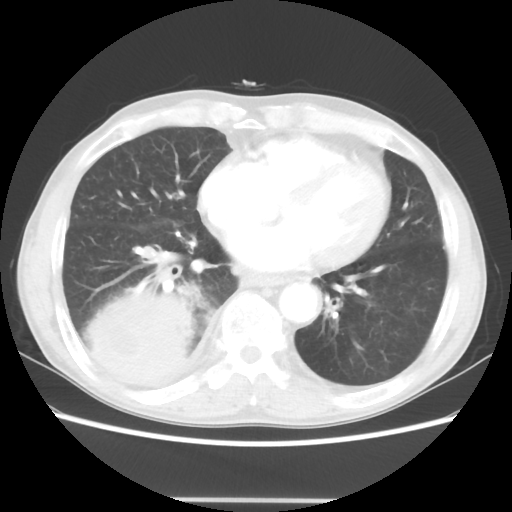
Chest CT, one axial slice. Slice 15 of 48 in the series (ordered by position). Reconstruction kernel STANDARD. Lung window (W 1500 / L -600 HU). 512 × 512 image matrix, field of view 361 × 361 mm. Male patient, age 66 years. From the clinical record (not read from this slice): clinical TNM (as recorded): T4 N1 M1.
Annotated regions visible in this slice (bounding box drawn by a radiologist):
- lung tumour (recorded histology: small cell carcinoma): box from (x=78, y=265) to (x=203, y=408) px